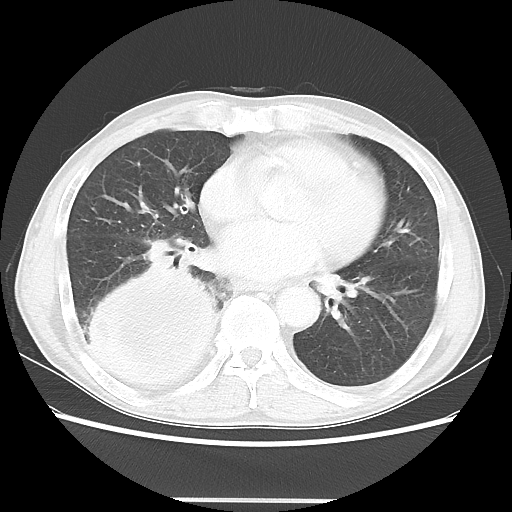
Chest CT, one axial slice. Slice 18 of 48 in the series (ordered by position). Reconstruction kernel LUNG. 100 kVp. Lung window (W 1500 / L -600 HU). 5 mm slice thickness. 512 × 512 image matrix, field of view 361 × 361 mm. Male patient, age 66 years. Case-level facts recorded for this patient, not image findings: clinical TNM (as recorded): T4 N1 M1; histopathological grade: G3.
Annotated regions visible in this slice (bounding box drawn by a radiologist):
- lung tumour (recorded histology: small cell carcinoma): bounding box <83,260,230,400> (left, top, right, bottom; pixels)